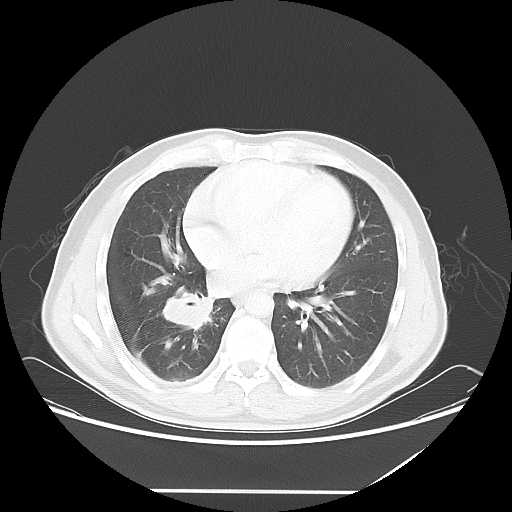
Chest CT, one axial slice. Slice 26 of 60 in the series (ordered by position). Reconstruction kernel LUNG. 120 kVp. Lung window (W 1500 / L -600 HU). 512 × 512 image matrix, field of view 419 × 419 mm. Patient: male, 48 years. Case-level facts recorded for this patient, not image findings: clinical TNM (as recorded): T3 N3 M1a.
Annotated regions visible in this slice (rectangle marked by the reading radiologist):
- lung tumour (recorded histology: squamous cell carcinoma): bounding box (x1, y1, x2, y2) in pixels: (158, 285, 215, 332)